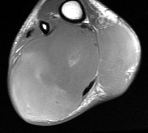
MRI of an extremity soft-tissue mass, one axial slice. Slice 30 of 76 in the series (ordered by position). MR volume resampled by the dataset authors to the PET/CT grid (not the native acquisition matrix). 148 × 133 image matrix. Male patient. Case-level facts recorded for this patient, not image findings: histological type: liposarcoma - round cell; grade: high; site of the primary tumour: right calf.
Structures marked on this image (expert contour drawn on MRI and transferred to this co-registered scan by the dataset authors):
- gross tumour volume (mass): bounding box [x1, y1, x2, y2] px = [13, 21, 137, 116]